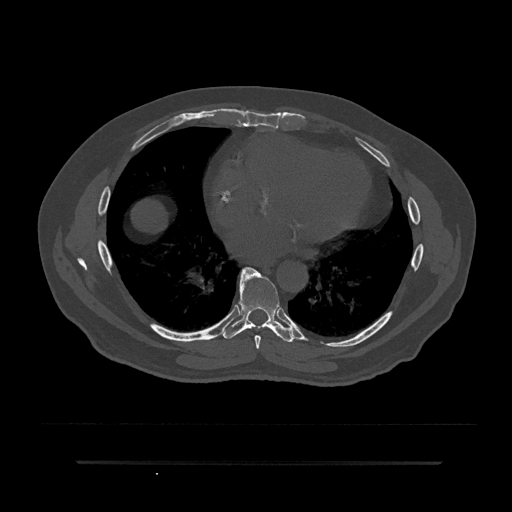
CT including the spine, one axial slice; slice 445 of 797 in the series (ordered by position); 120 kVp; bone window (W 1800 / L 400 HU); 512 × 512 image matrix, field of view 464 × 464 mm. Male patient, age 59 years. From the clinical record (not read from this slice): primary cancer: bile ducts; vertebrae with lytic lesions (as recorded): T10.
Outlined on this slice (semi-automatically segmented with operator editing):
- T7 vertebra: bounding box [x1, y1, x2, y2] px = [241, 267, 261, 349]
- T8 vertebra: [222, 269, 295, 342]